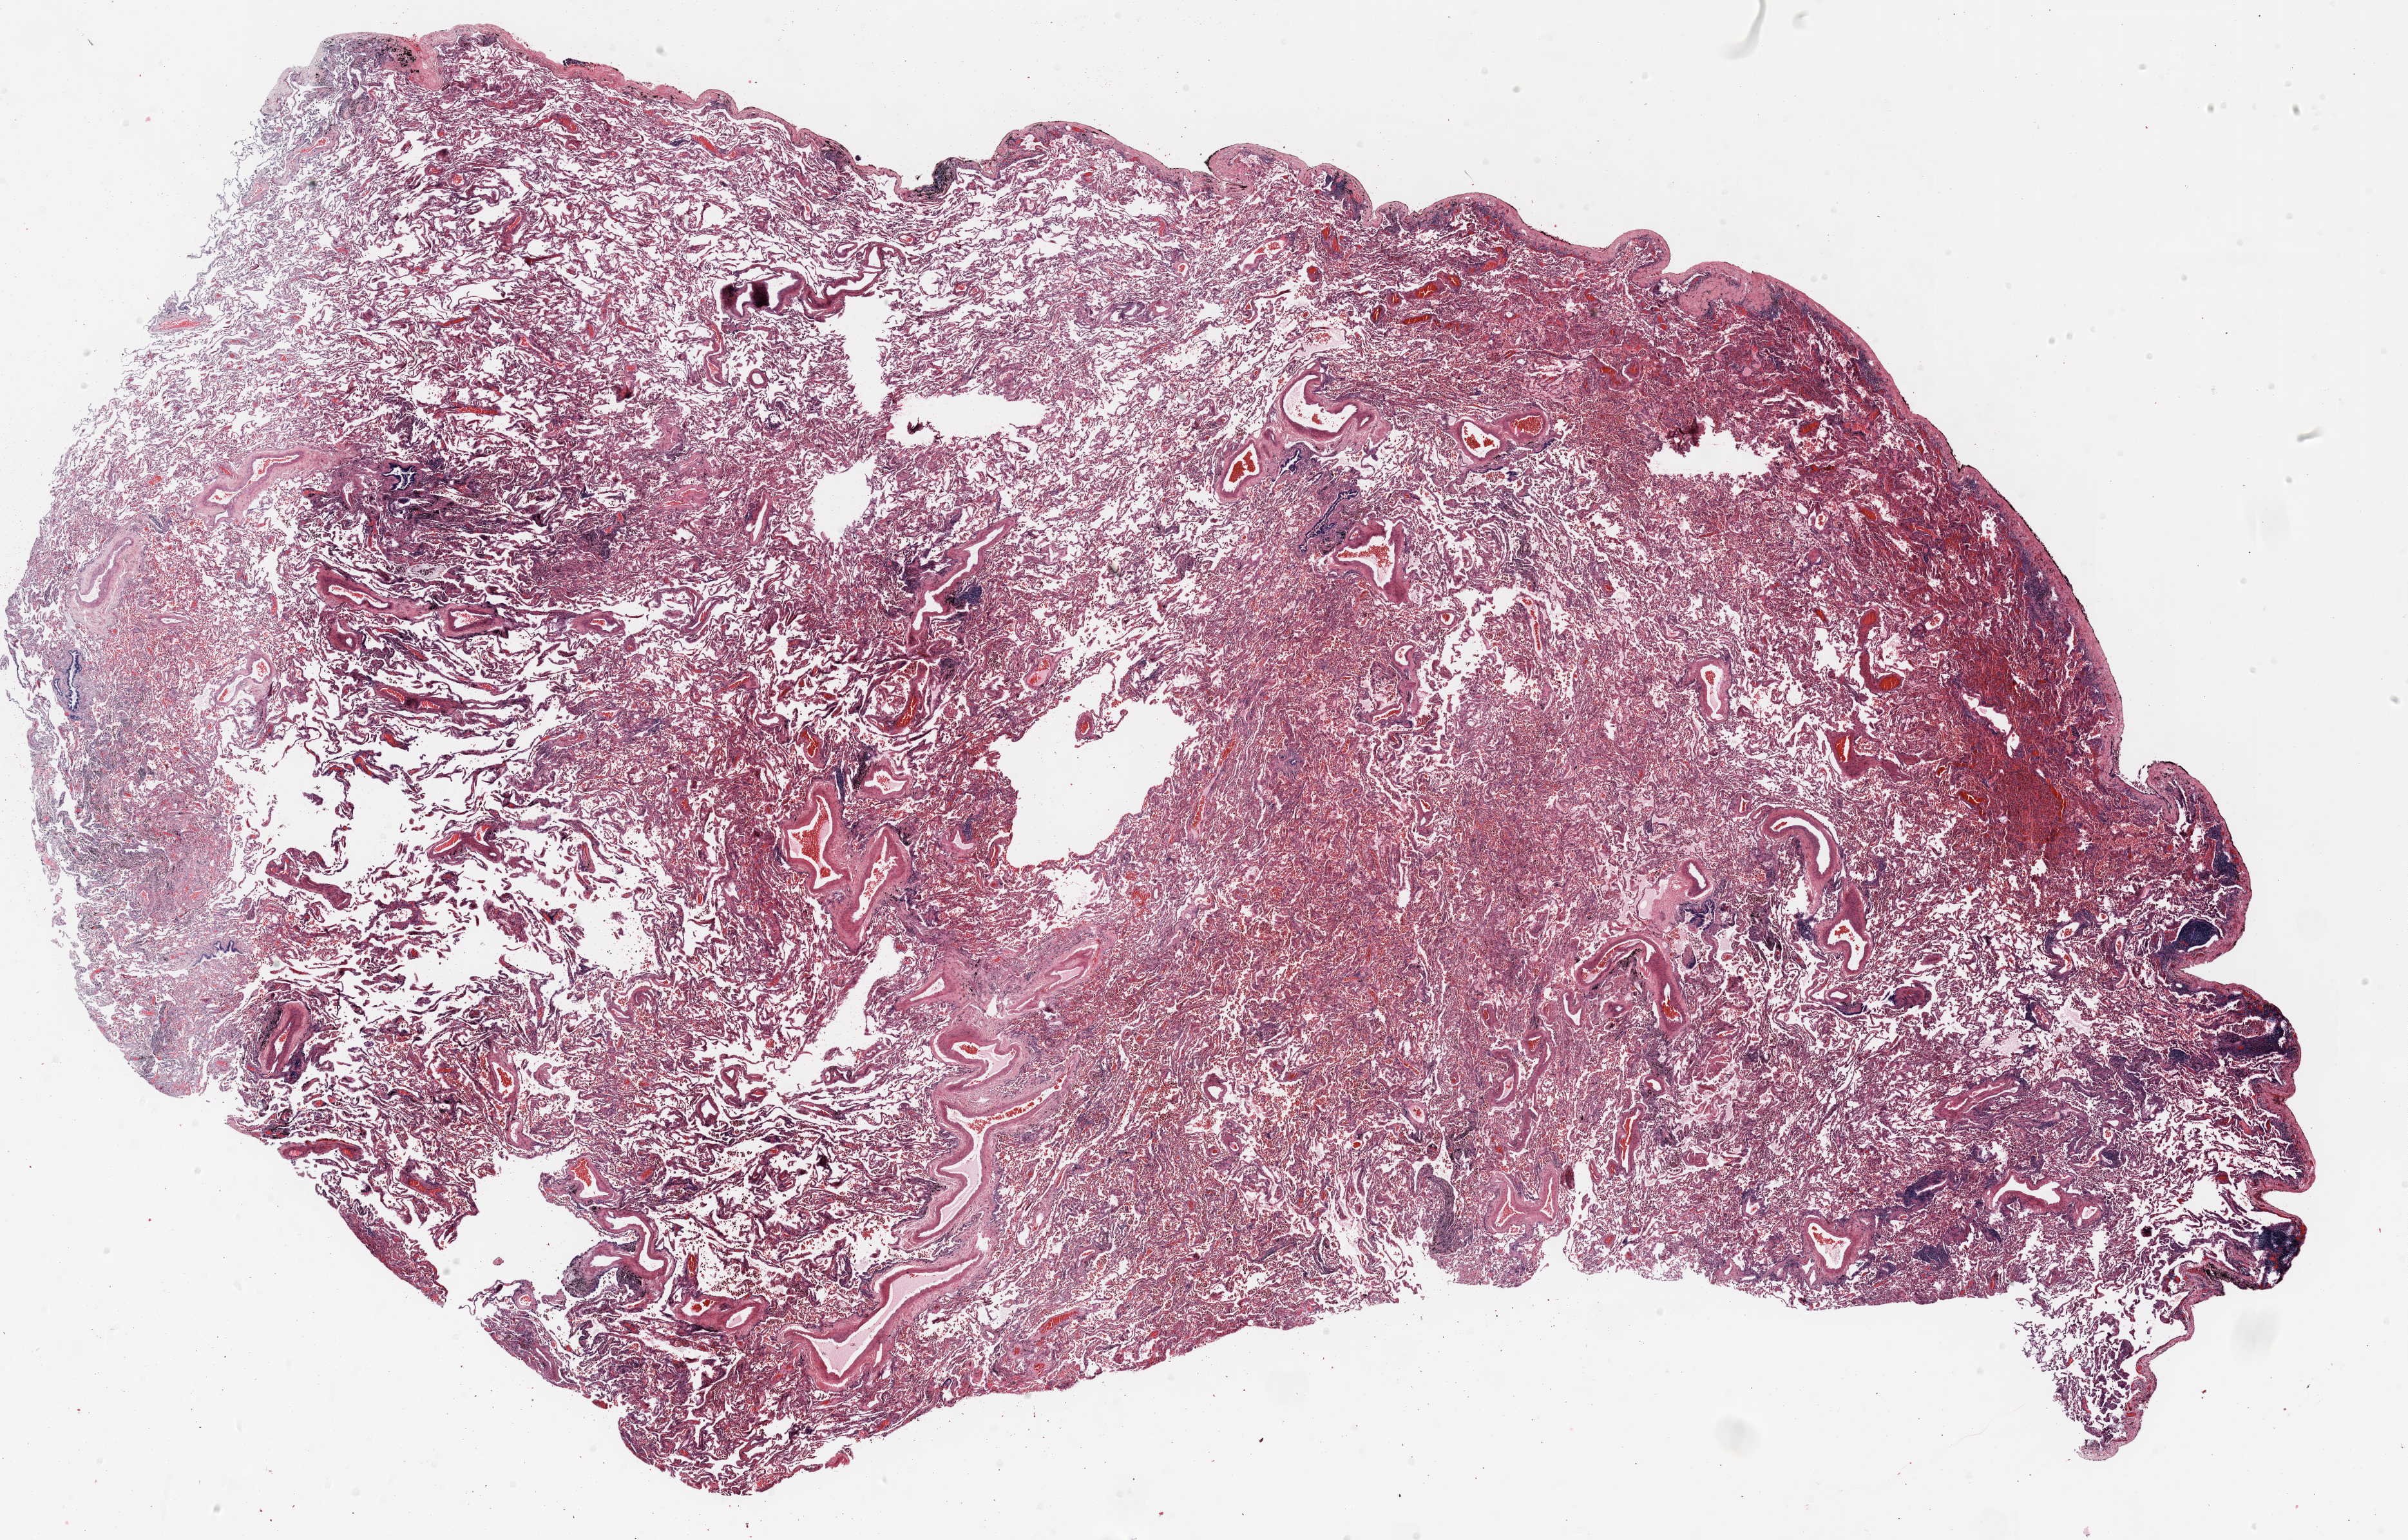
H&E-stained whole-slide image — whole scanned area (about 30.0 x 19.2 mm, slide scanned at 20x) shown as a low-resolution overview. Formalin-fixed paraffin-embedded (FFPE) section. Lung tissue. Male patient, aged 66 at enrolment. Grade: poorly differentiated (G3).
Stage (AJCC 6th edition): IIB. Tumour size (pathology): 50 mm. Primary tumour location (clinical record): right upper lobe. Participant's lung-cancer diagnosis: Squamous cell carcinoma, adenoid.